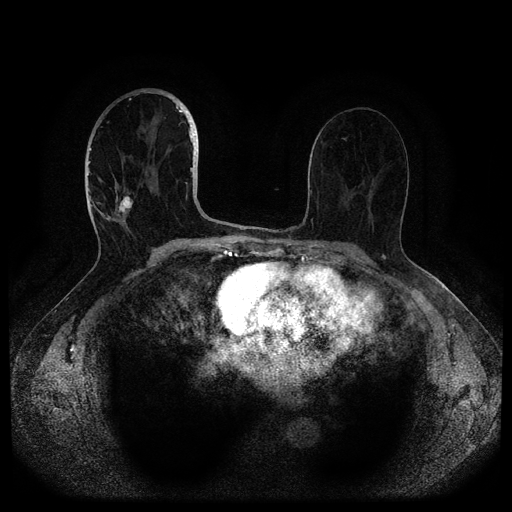
Breast MRI (dynamic contrast-enhanced, multi-phase), one axial slice; position 53 of 116 along the scan axis; dynamic contrast-enhanced series, time point 2 of 5 at this slice position (early post-contrast); 1.5 T; TE 2.6 ms, TR 5.3 ms; 2 mm slice thickness; 512 × 512 image matrix, field of view 350 × 350 mm. Patient: female, 82 years.
Outlined on this slice (semi-automatically segmented with operator editing):
- breast lesion (labelled 'tumour' in the annotation; benign lesions carry a separate 'benign' label): bounding box [x1, y1, x2, y2] px = [115, 192, 133, 218]